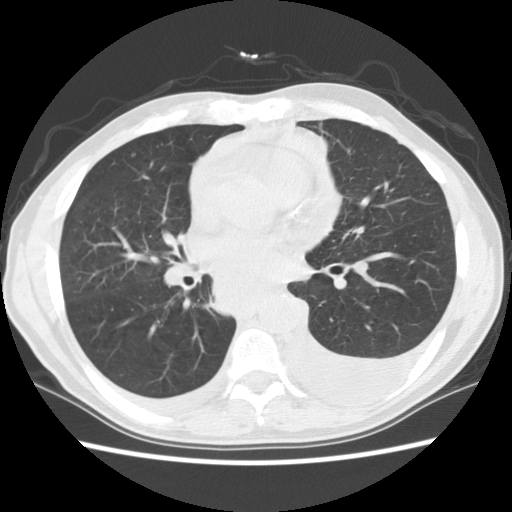
Chest CT (low-dose screening protocol), one axial image. Baseline screening round. Lung window (W 1500 / L -600 HU). 2.5 mm slice thickness. Slice 61 of 135 in the series. Male, age 60 years at enrolment. Current smoker at enrolment.
• Lesion marked by an expert reader, box from (x=174, y=241) to (x=306, y=333) px.
• Screening reader's record for this exam: no non-calcified nodule ≥4 mm recorded.
• Official screen result: negative screen, significant abnormalities not suspicious for lung cancer.
• Lung cancer was diagnosed 12 days after this screen: squamous cell carcinoma, NOS, carina, poorly differentiated (G3), stage IV (AJCC 6th edition).